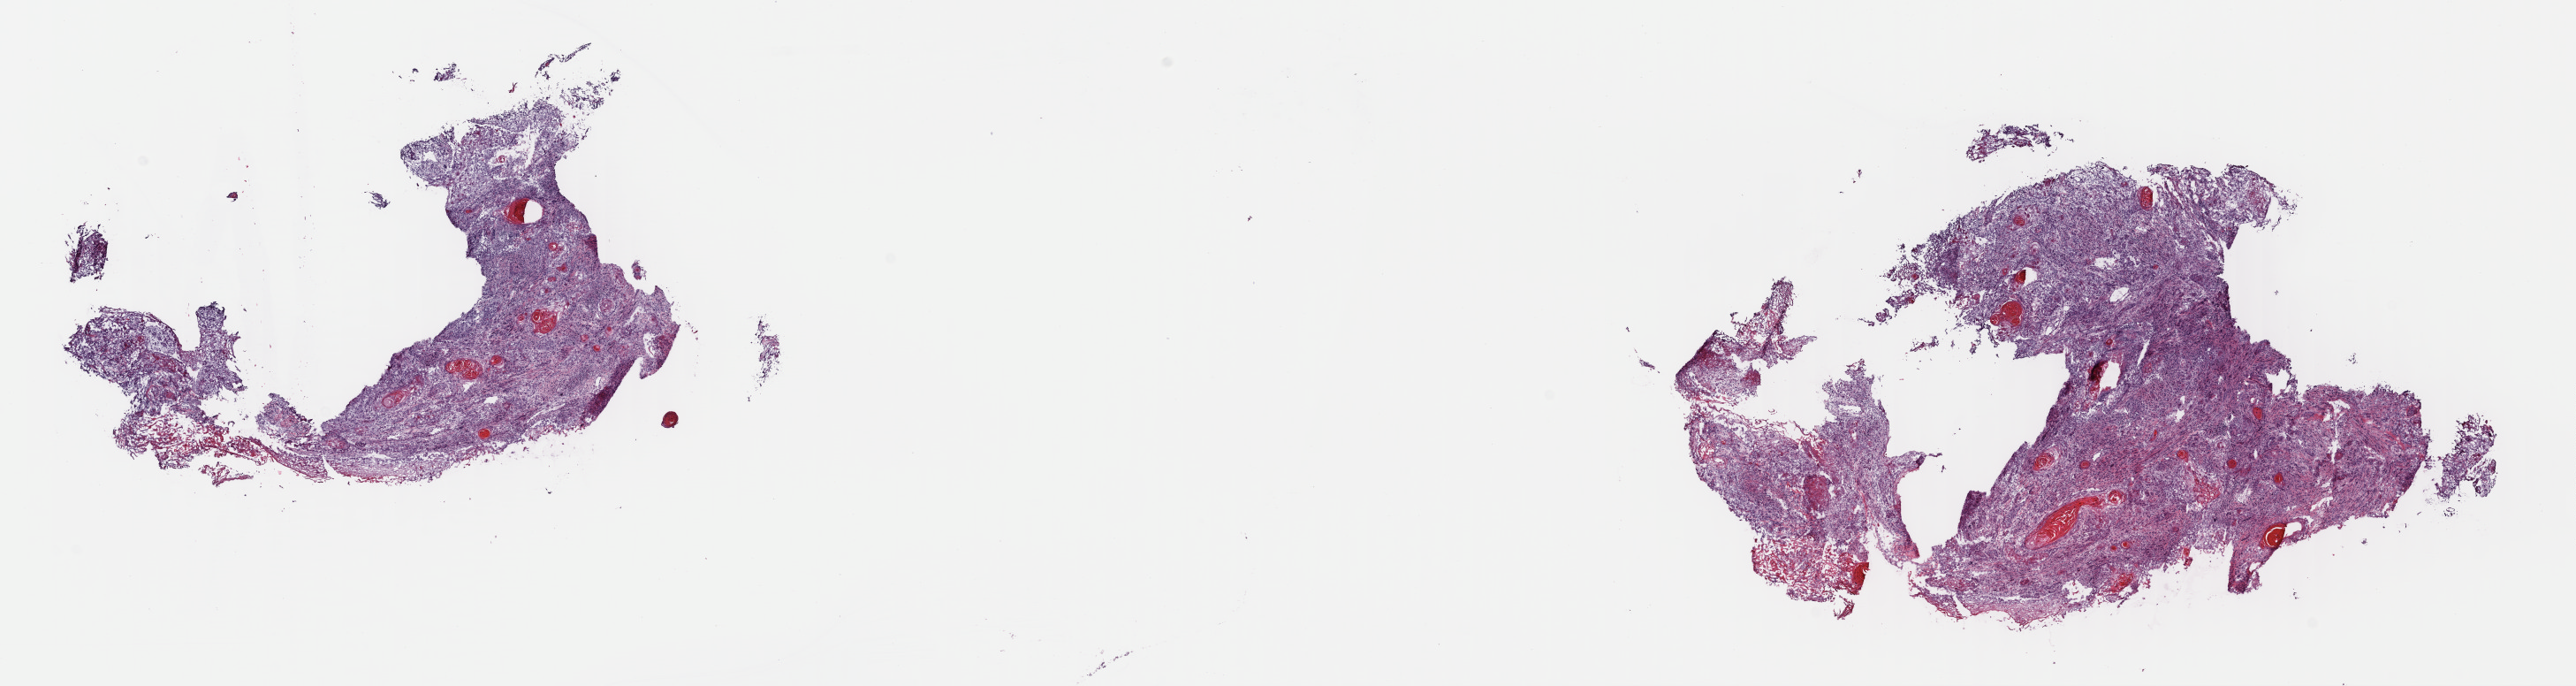
Hematoxylin and eosin (H&E) stained whole-slide image — whole scanned area (about 22.9 x 6.1 mm) shown as a low-resolution overview, frozen section from the top of the tissue portion, primary tumour sample from the head and neck. Male, age 49 years at initial diagnosis. Histologic grade: G2 (moderately differentiated). Slide review estimates, as recorded: tumour cells 75%, tumour nuclei 75%, normal cells 0%, stromal cells 25%, necrosis 0%. Inflammatory infiltration, as recorded: lymphocyte infiltration 5%, monocyte infiltration 0%, neutrophil infiltration 0%.
Pathologic diagnosis: Squamous cell carcinoma, NOS (tongue, NOS).